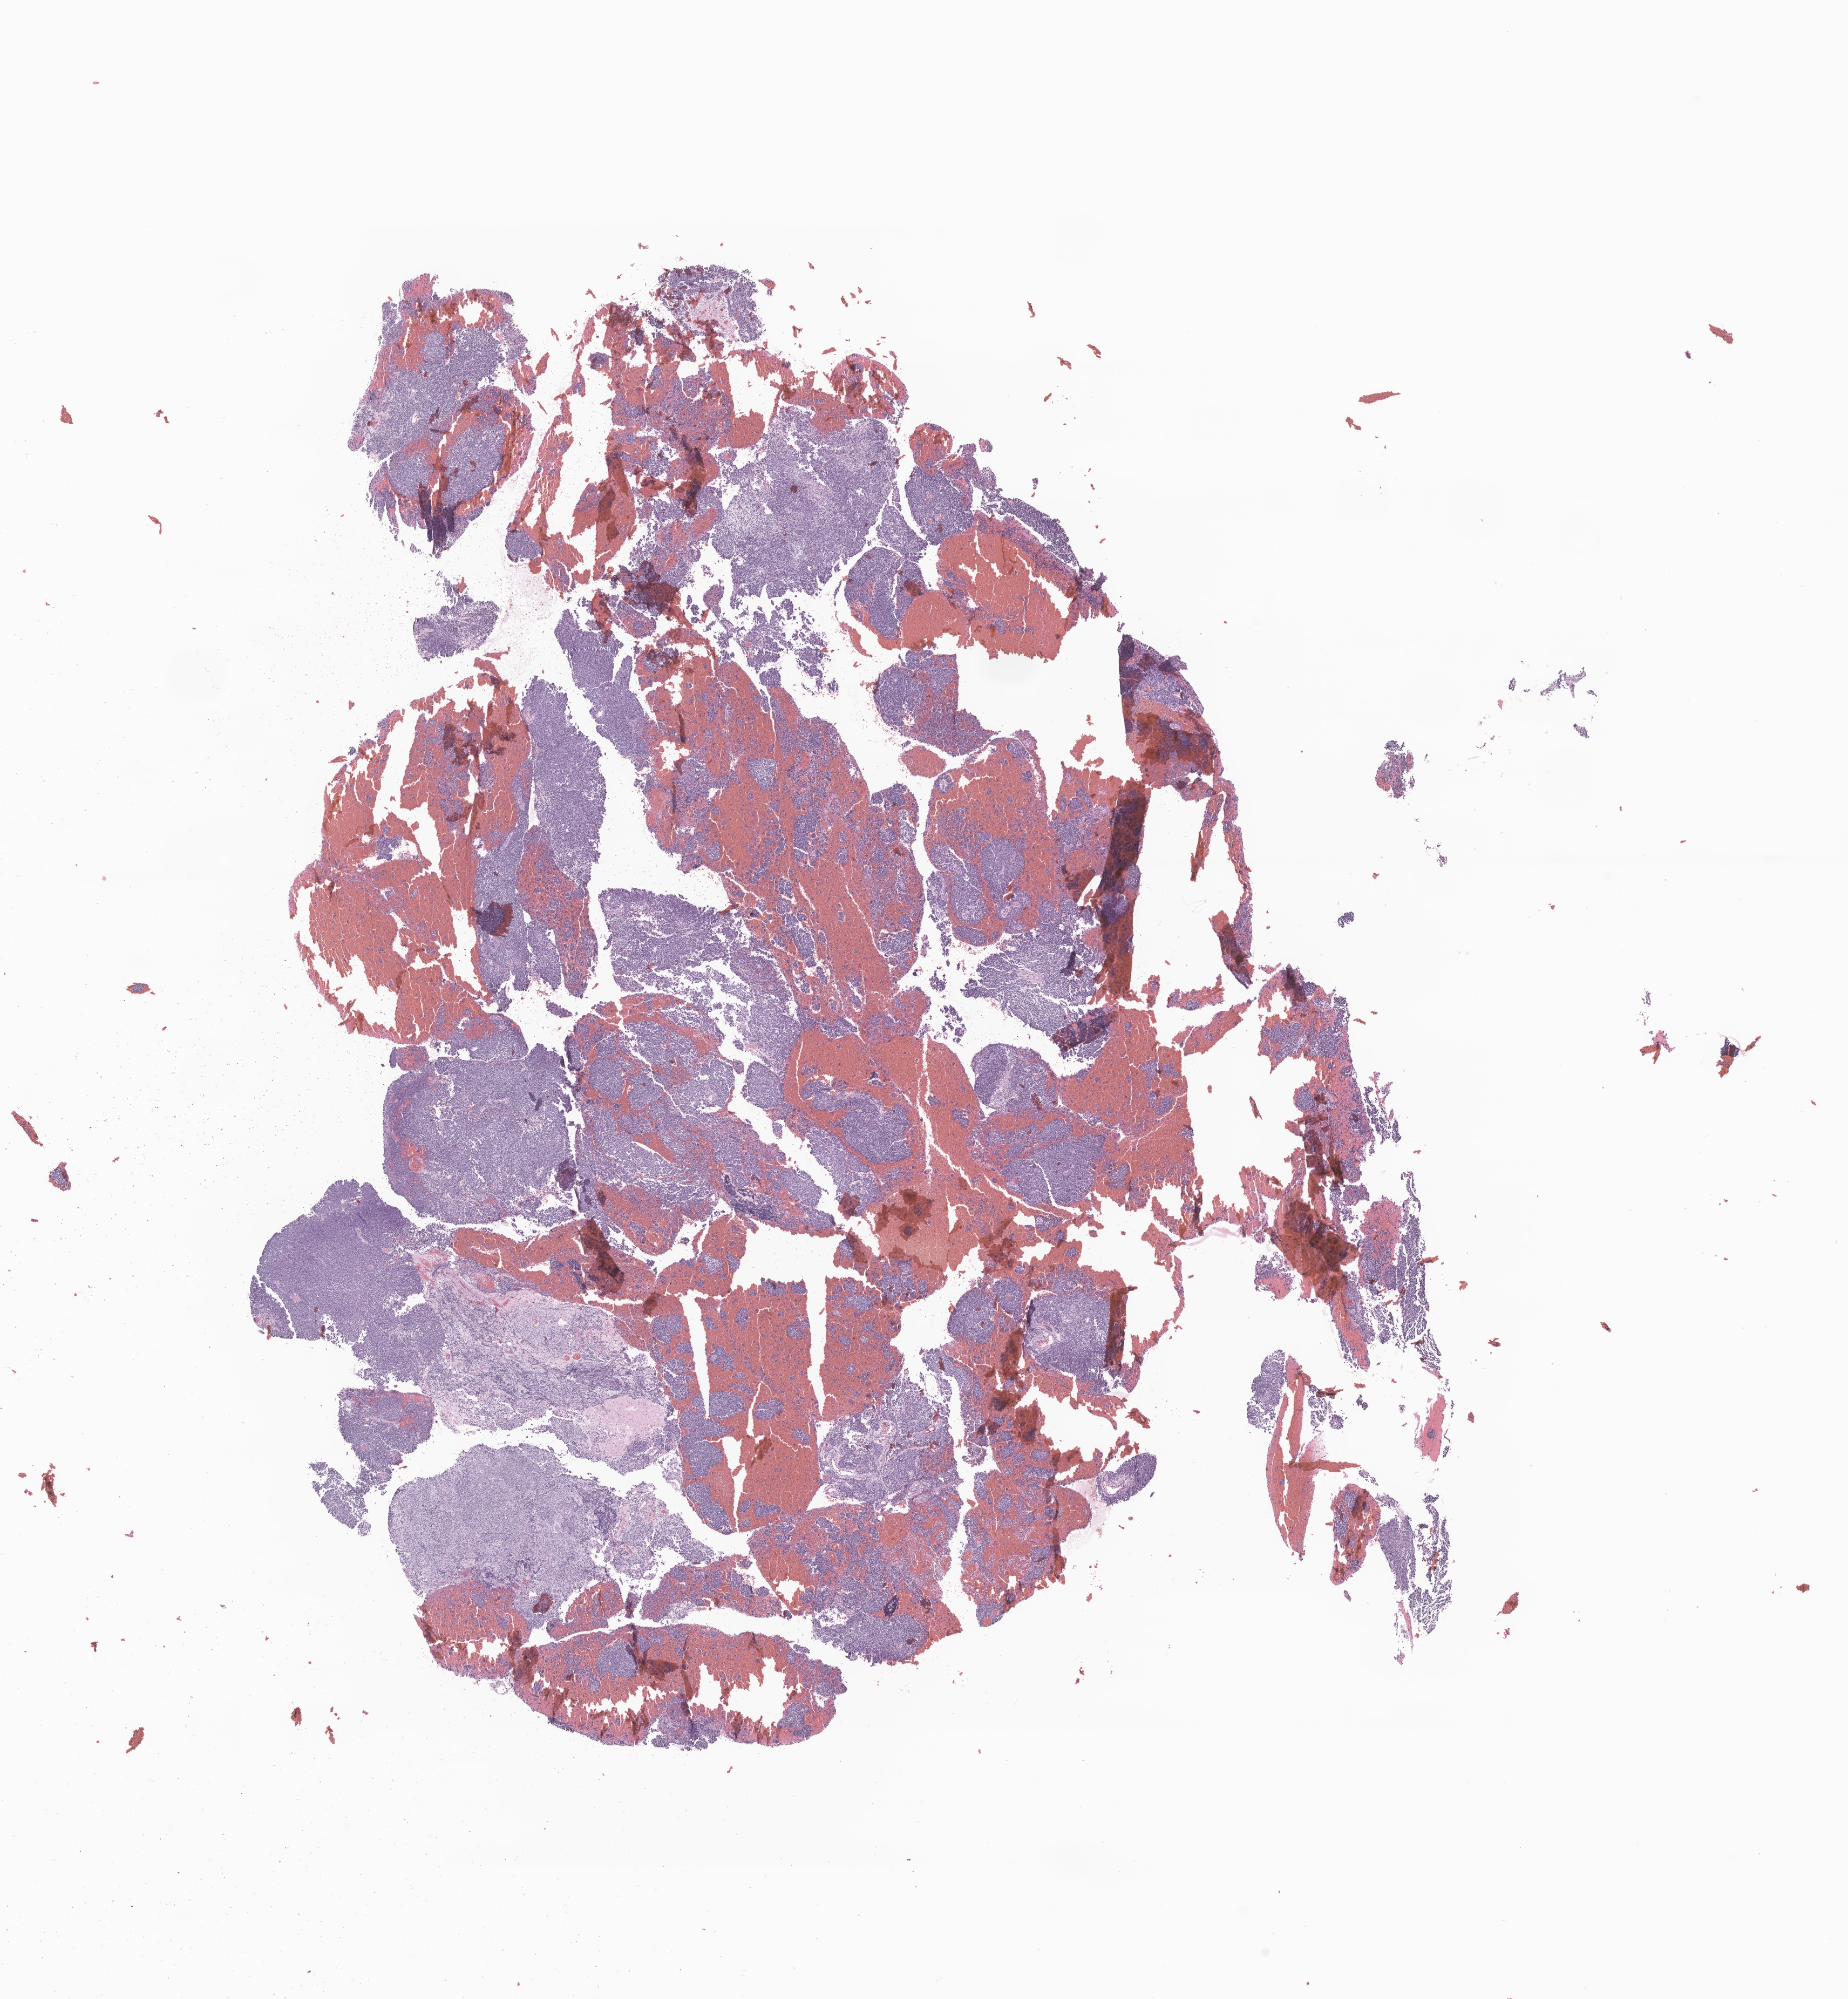
Whole-slide image, H&E stain of tumor tissue from the brain — whole scanned area (about 14.4 x 15.6 mm) shown as a low-resolution overview; FFPE section. Female patient, age 635 days (about 1.7 years).
Diagnosis: Medulloblastoma, NOS.